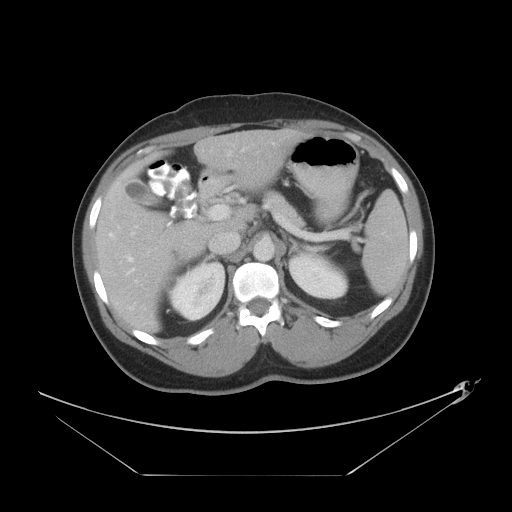
Contrast-enhanced abdominal CT, one axial slice. Slice 25 of 44 in the series (ordered by position). Reconstruction kernel STANDARD. Intravenous contrast given. Soft-tissue window (W 400 / L 40 HU). 5 mm slice thickness. 512 × 512 image matrix. Male patient, age 49 years. From the clinical record (not read from this slice): diagnosis: colorectal cancer liver metastases, imaged before liver resection; multiple liver metastases: no; largest metastasis: 8.5 cm.
Structures marked on this image (manually delineated by an expert):
- hepatic veins: box from (x=128, y=152) to (x=230, y=262) px
- liver: (x=96, y=130)–(x=307, y=333)
- planned liver remnant (the part of the liver to remain after resection): (x=124, y=130)–(x=308, y=231)
- portal vein (with intrahepatic branches): (x=109, y=204)–(x=230, y=272)